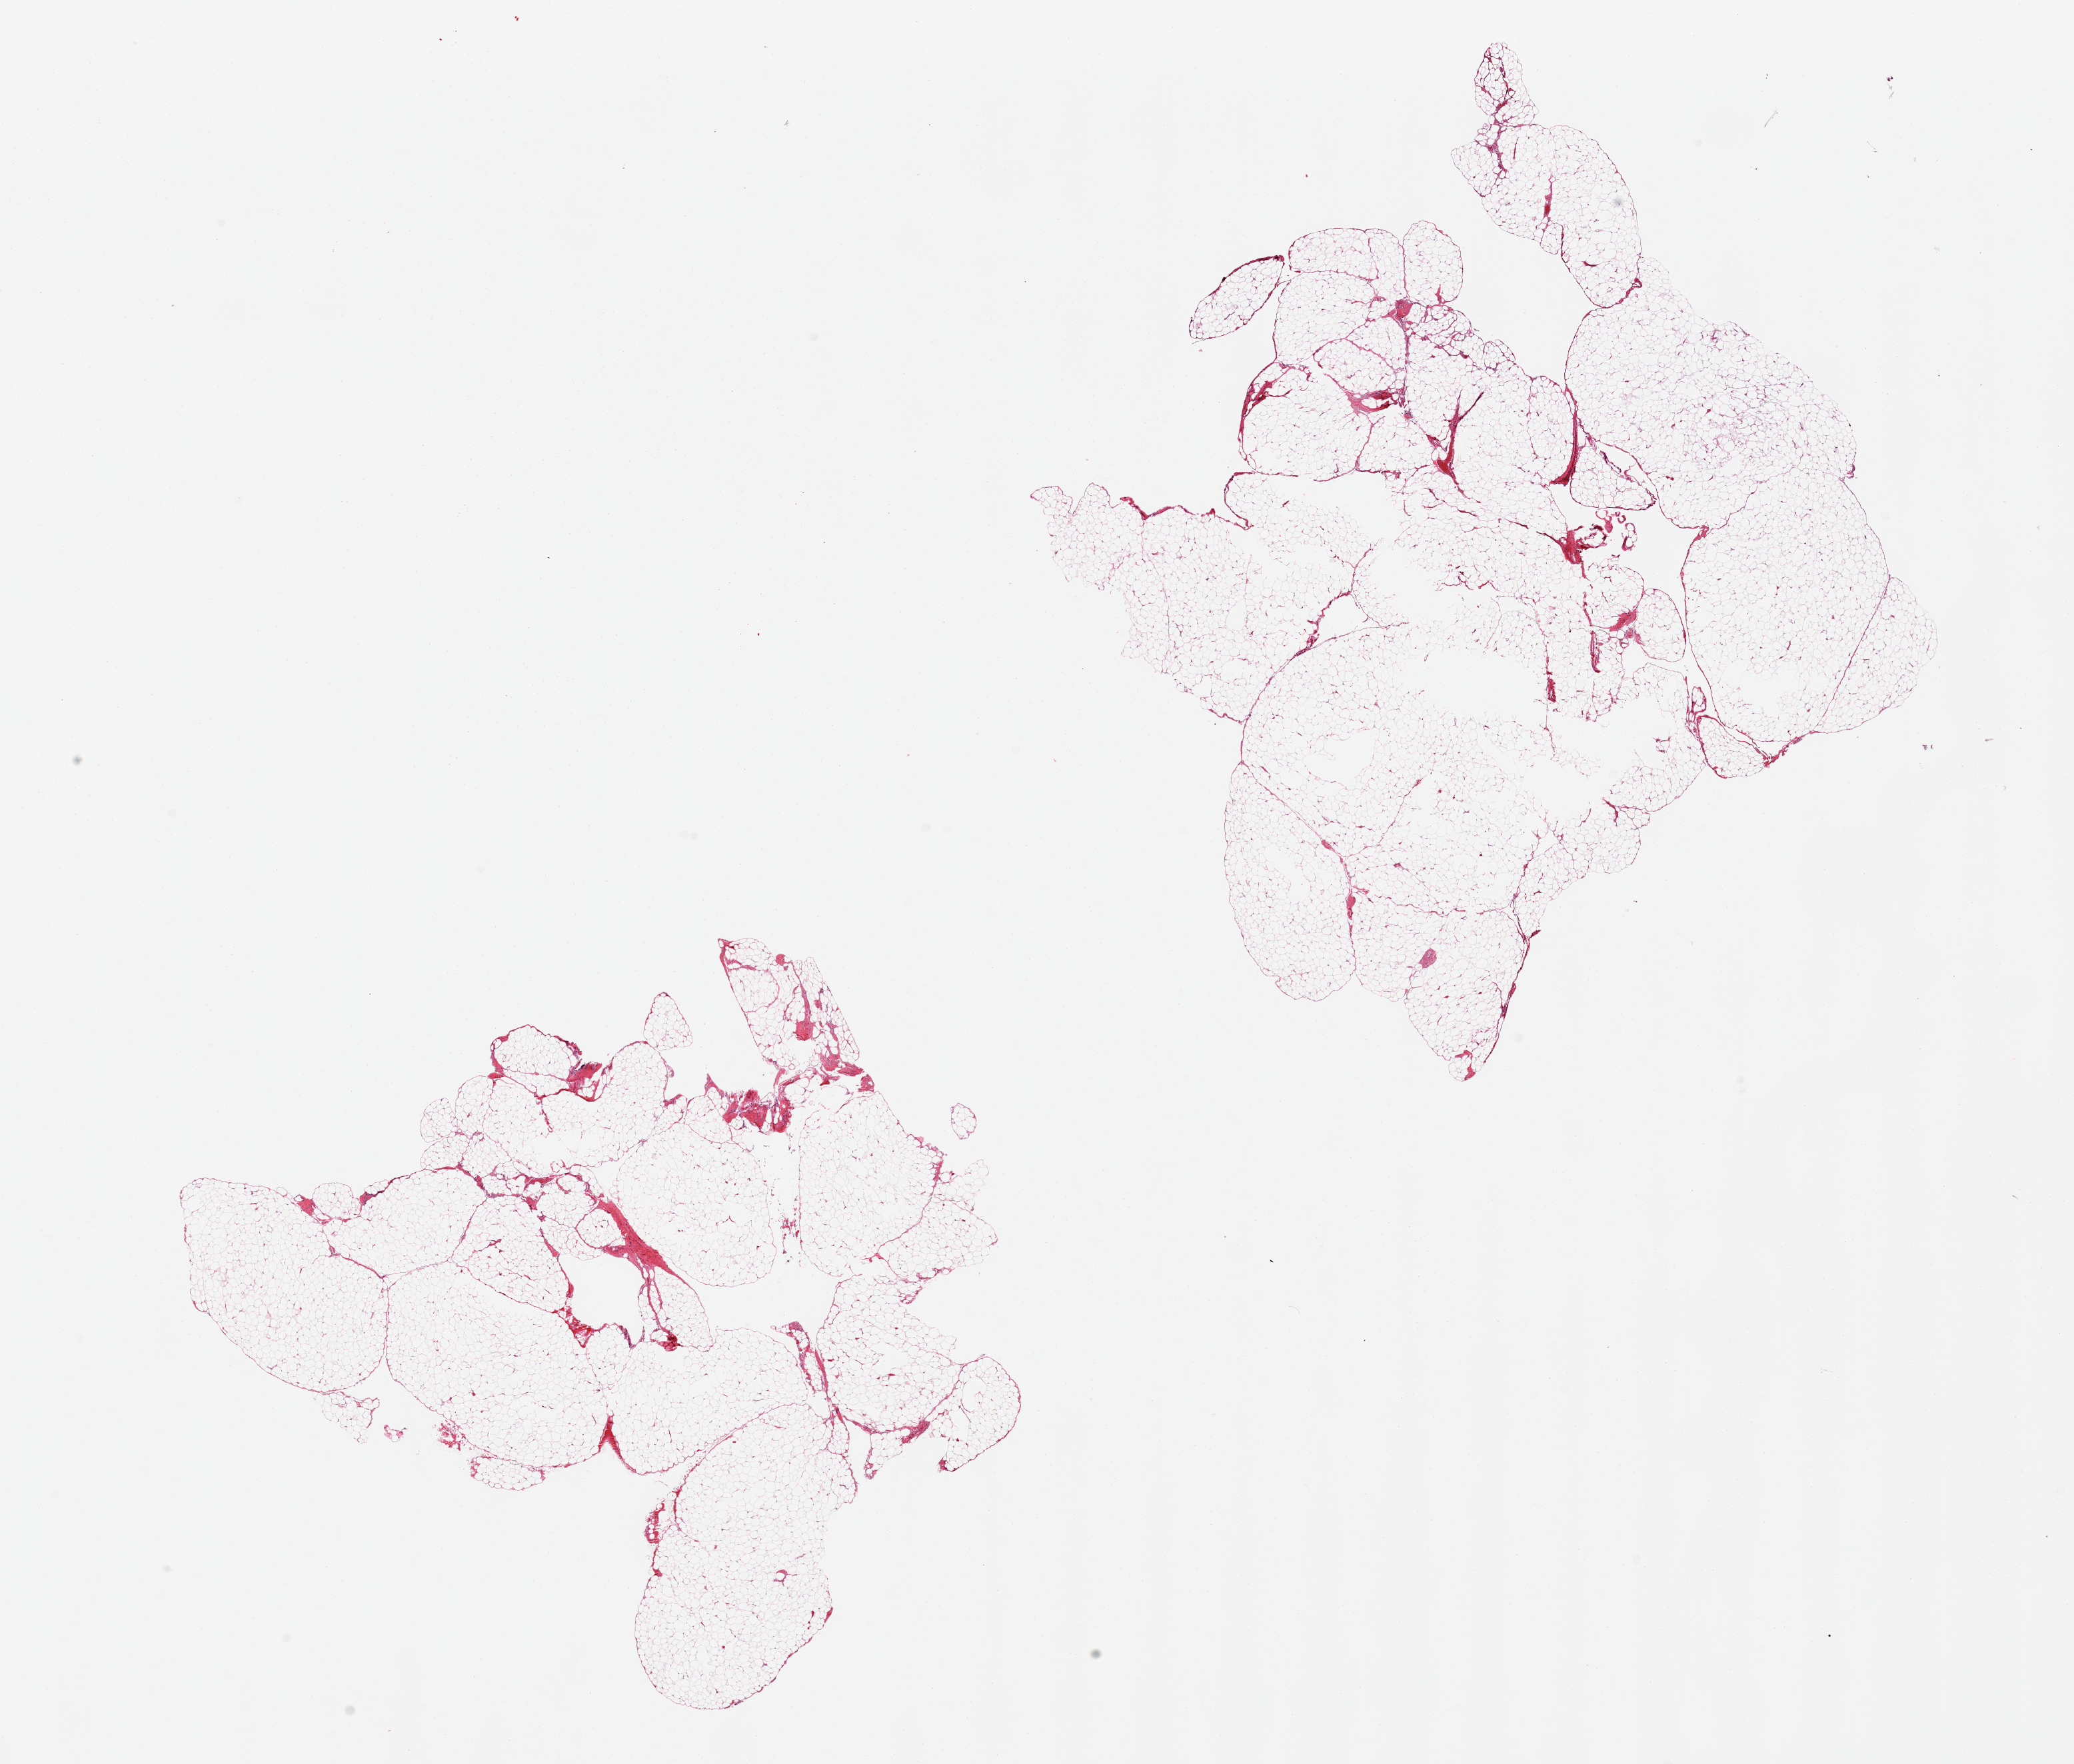
Whole-slide image, hematoxylin and eosin (H&E) stain, brightfield — low-resolution overview of the scanned area, about 24.6 x 20.9 mm; PAXgene-fixed paraffin-embedded (PFPE) section; section of omentum (target tissue); tissue donor sample. Male donor.
Review note (as recorded): 2 pieces, ~10% fibrous/vascular tissue.